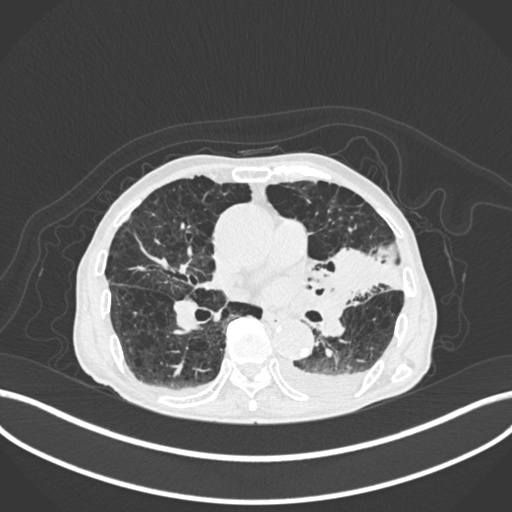
Chest CT, one axial slice. Slice 109 of 400 in the series (ordered by position). 120 kVp. Lung window (W 1500 / L -600 HU). 1 mm slice thickness. 512 × 512 image matrix. Patient: male, 90 years or older. Case-level facts recorded for this patient, not image findings: clinical TNM (as recorded): T2b N1 M0.
Structures marked on this image (bounding box drawn by a radiologist):
- lung tumour (recorded histology: squamous cell carcinoma): box from (x=330, y=236) to (x=386, y=292) px